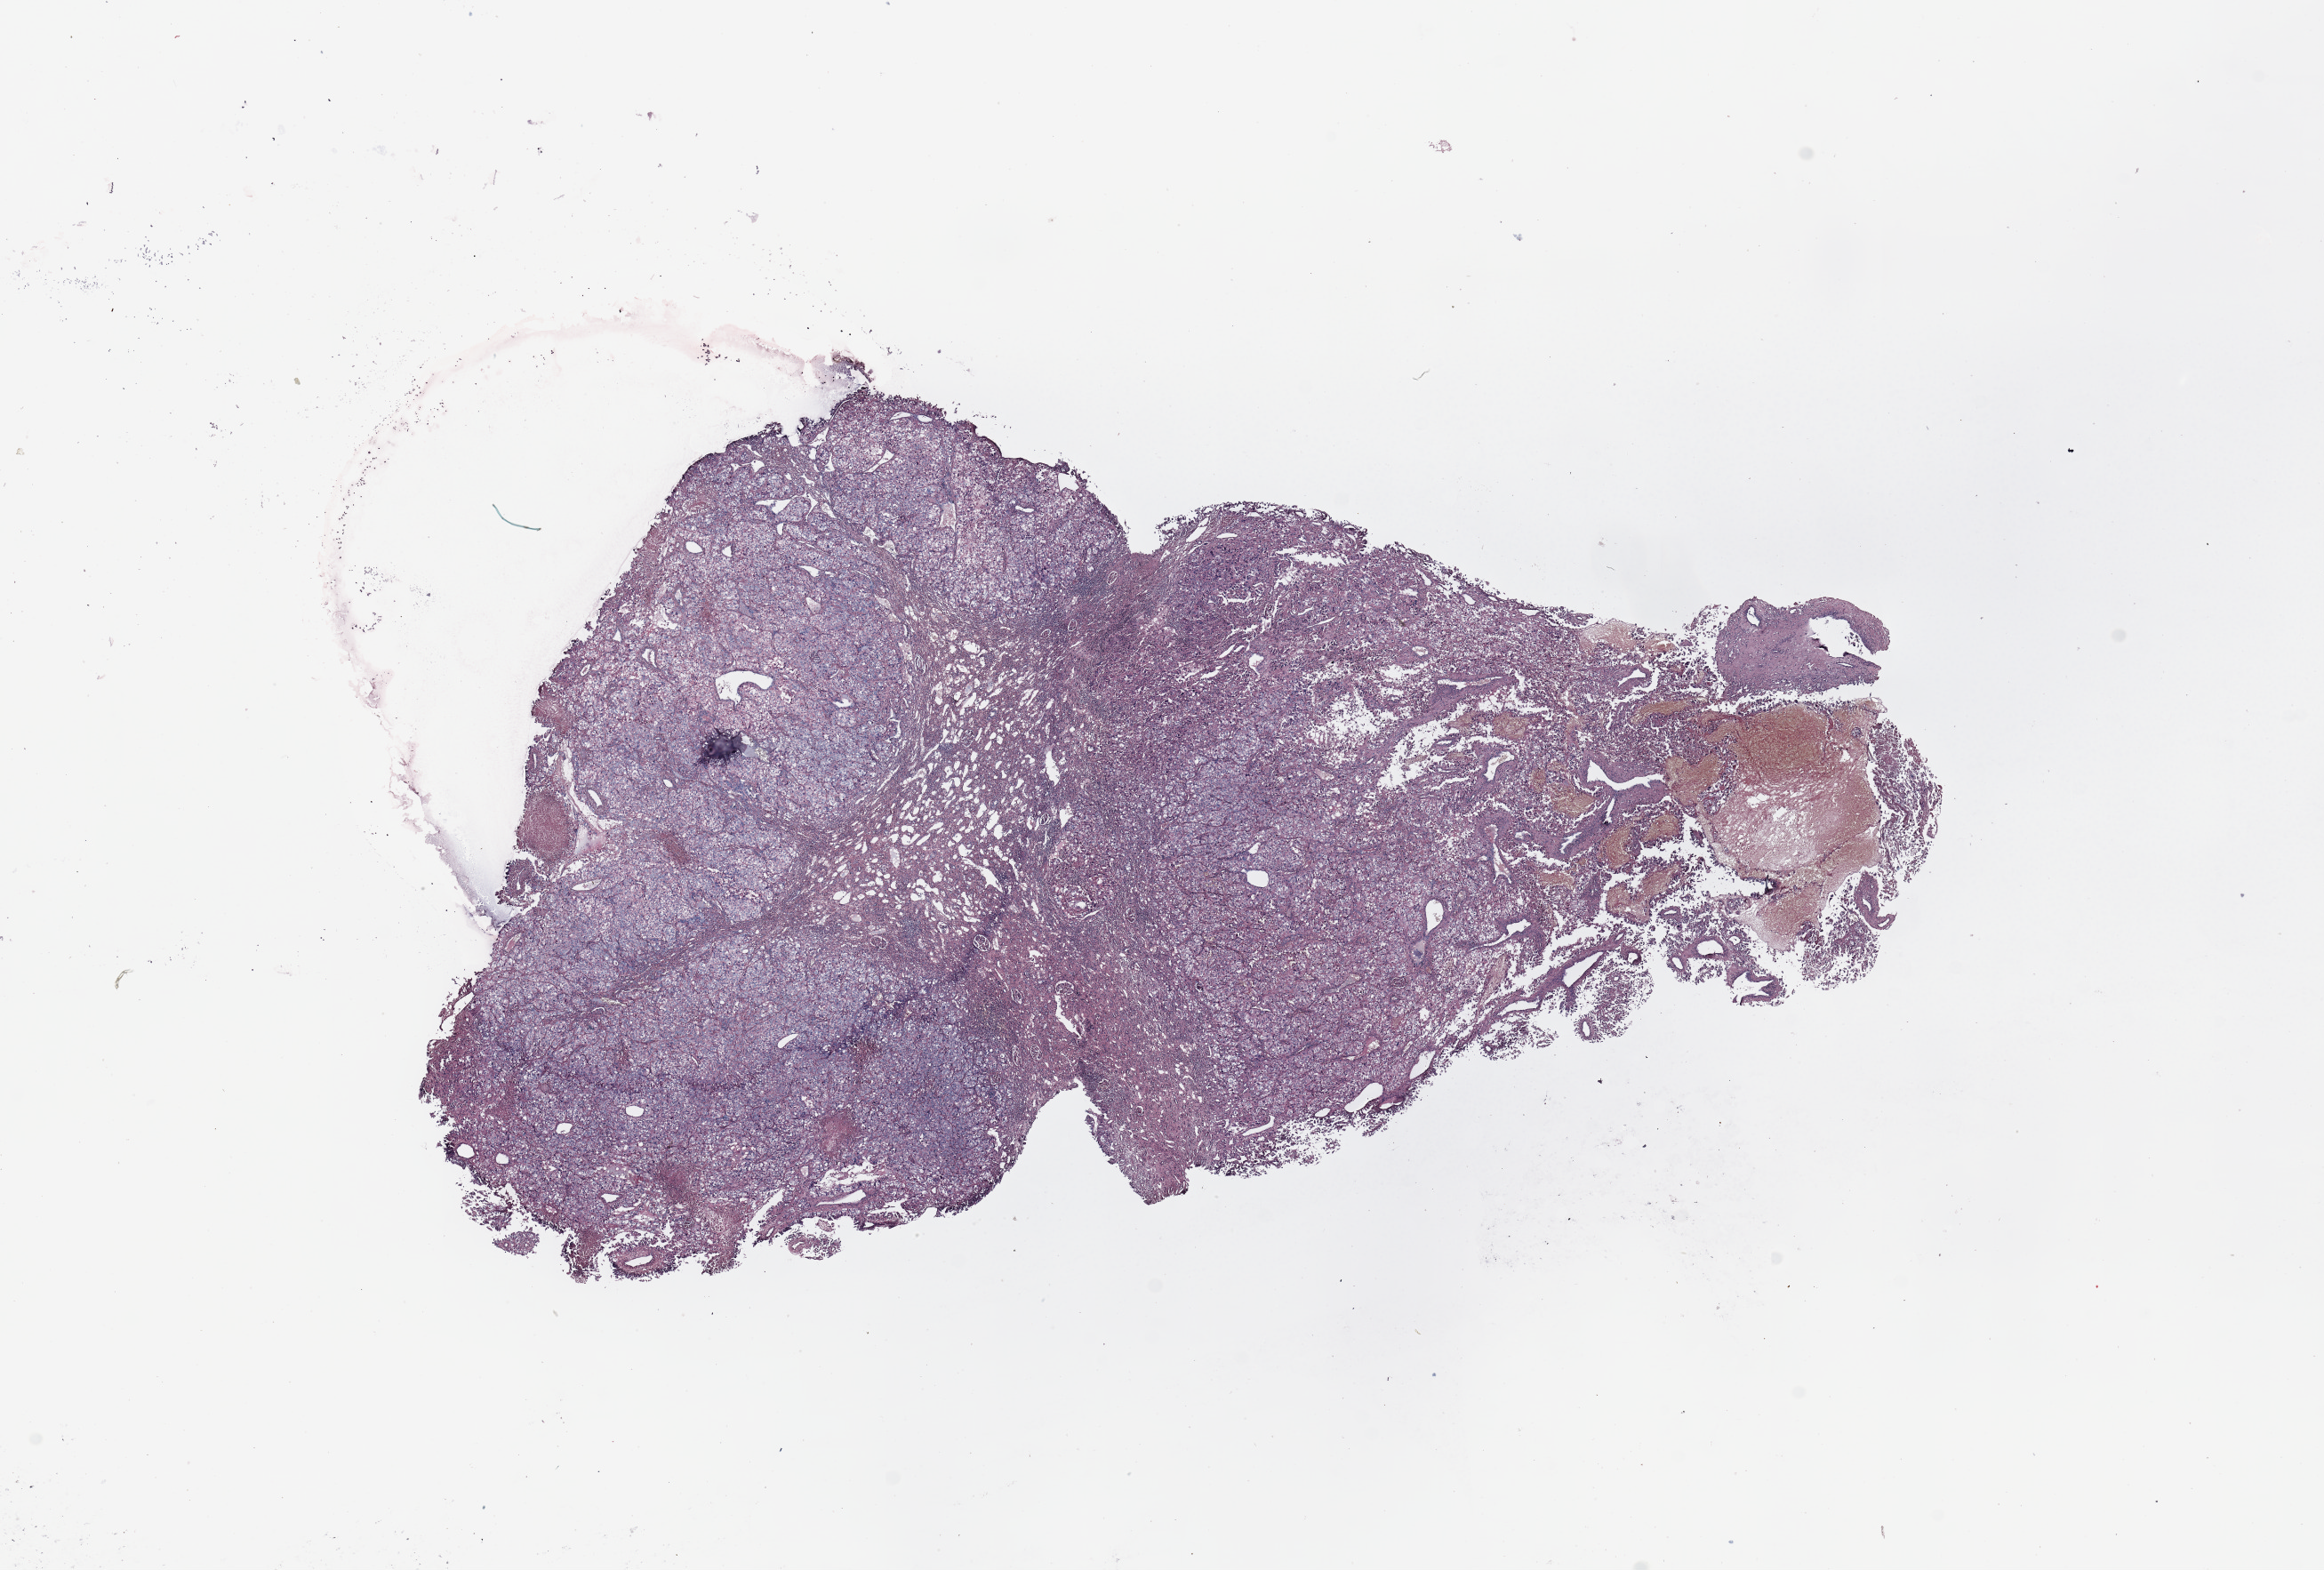
Digitized H&E tissue section (whole slide) — low-resolution overview of the scanned area, about 20.7 x 14.0 mm (from a 20x scan), tumour tissue sample, sampled site: kidney. Patient: female, age 56 years. Histologic grade: G3 (poorly differentiated). Composition of this section per pathologist review: tumour nuclei 90%, necrosis 5%.
AJCC pathologic stage: IV. Histologic diagnosis: Renal cell carcinoma, NOS.